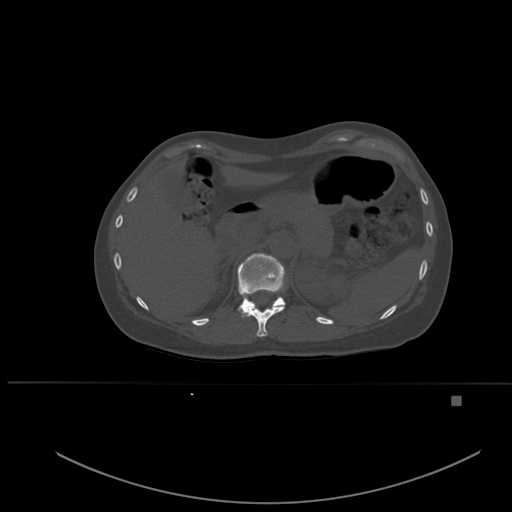
CT including the spine, one axial slice. Position 263 of 651 along the scan axis. Bone window (W 1800 / L 400 HU). 1.5 mm slice thickness. 512 × 512 image matrix, field of view 443 × 443 mm. Patient: female, 49 years. Case-level facts recorded for this patient, not image findings: primary cancer: breast; vertebrae with lytic lesions (as recorded): L3, T12, L4.
Structures marked on this image (semi-automatically segmented with operator editing):
- T11 vertebra: box from (x=243, y=306) to (x=285, y=337) px
- T12 vertebra: (x=237, y=253)–(x=286, y=317)